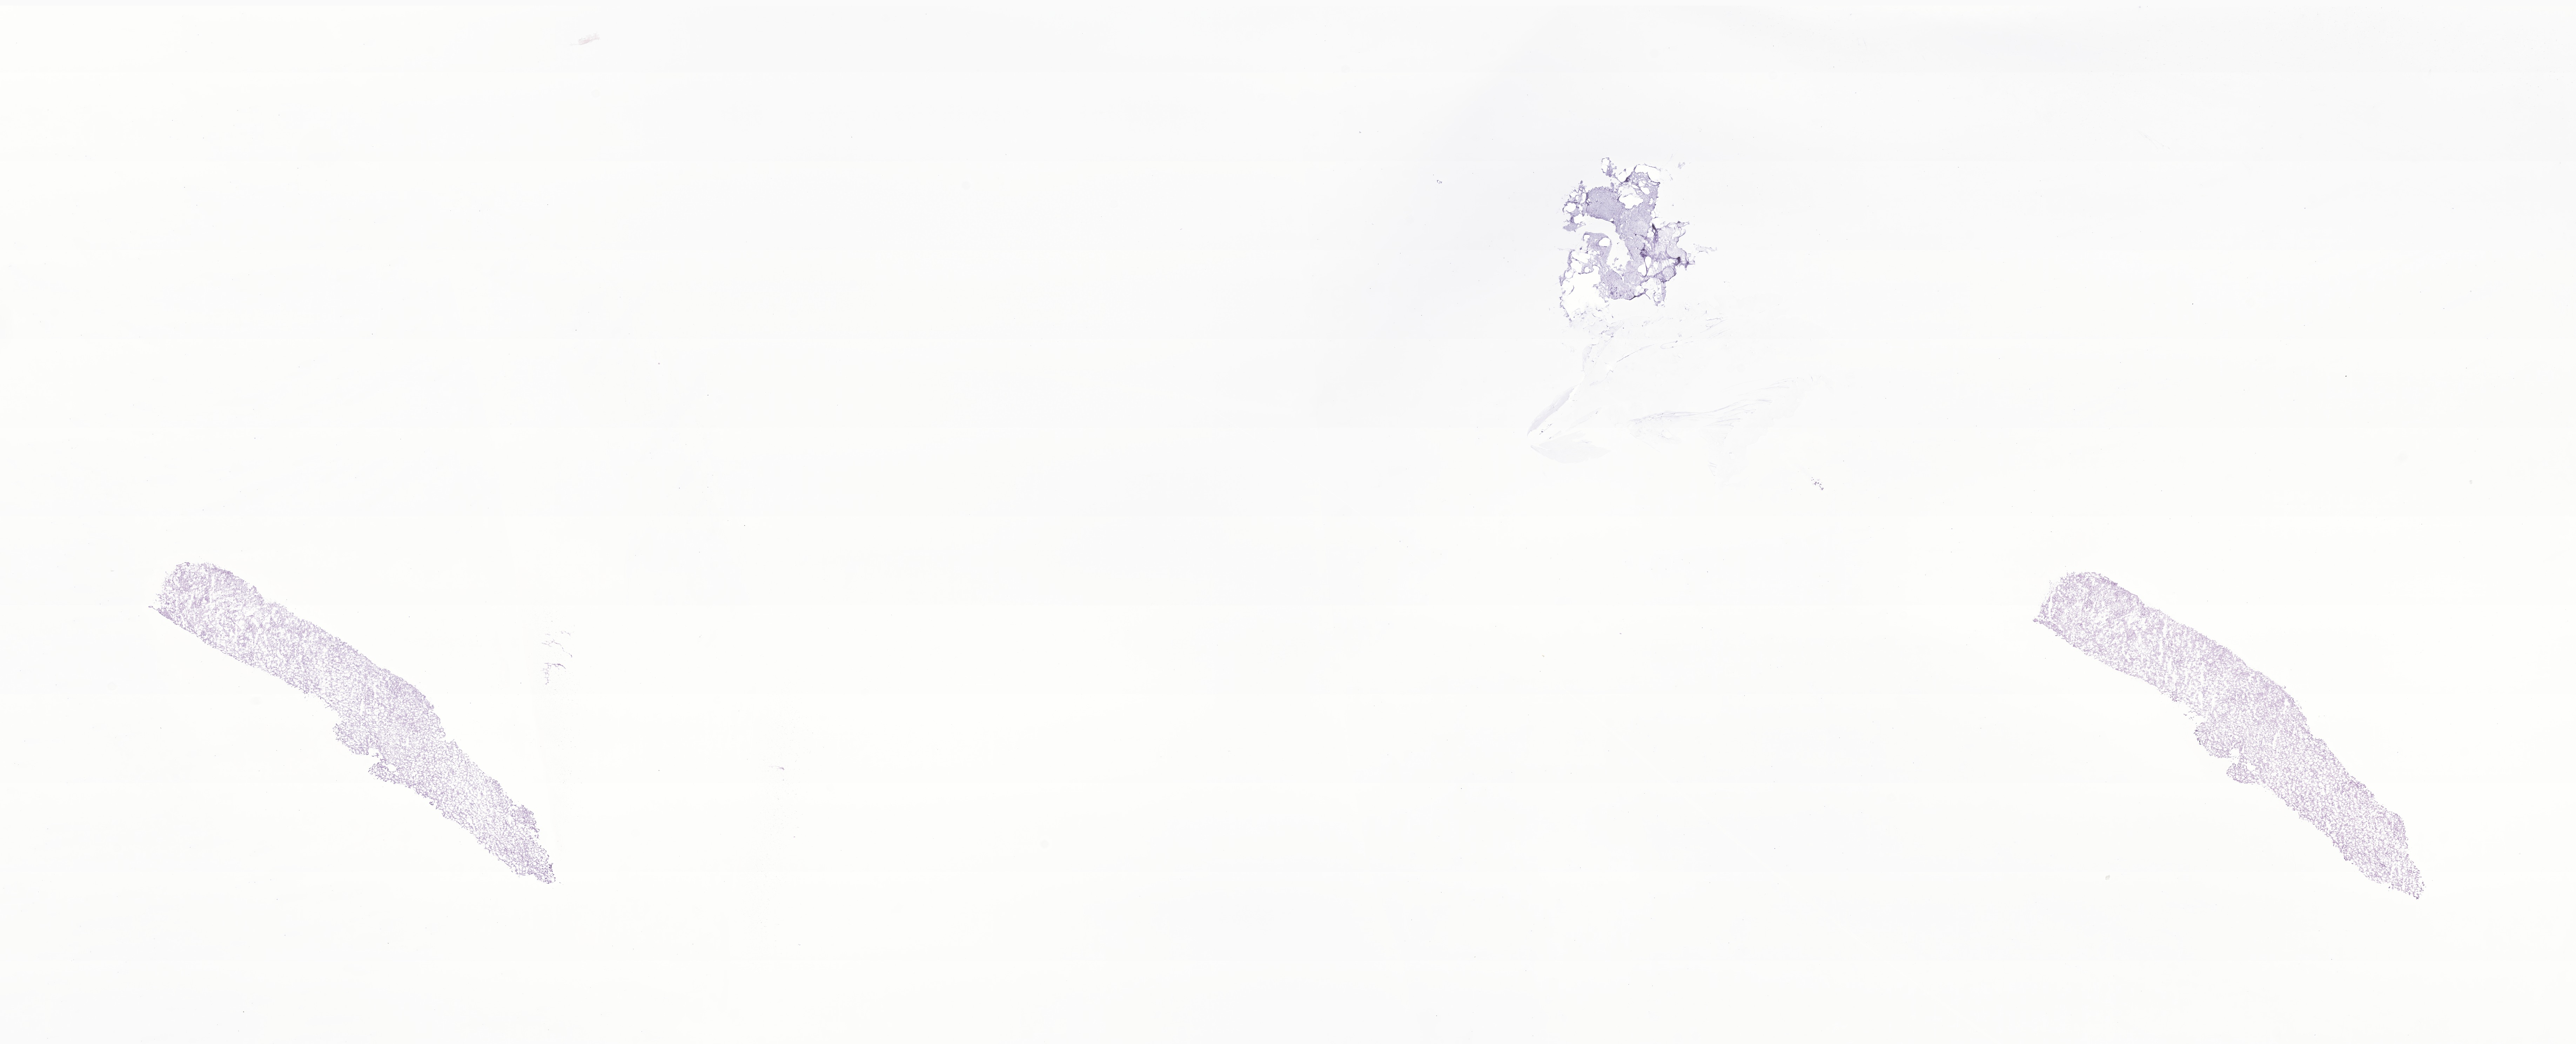
Digitized haematoxylin and eosin-stained section of tumor tissue from the brain, a low-resolution overview of the entire scanned area, about 31.0 x 12.5 mm, cryosection (OCT / tissue freezing medium). Patient male; age 39 months (3 years 3 months).
- recorded diagnosis: Pilocytic astrocytoma